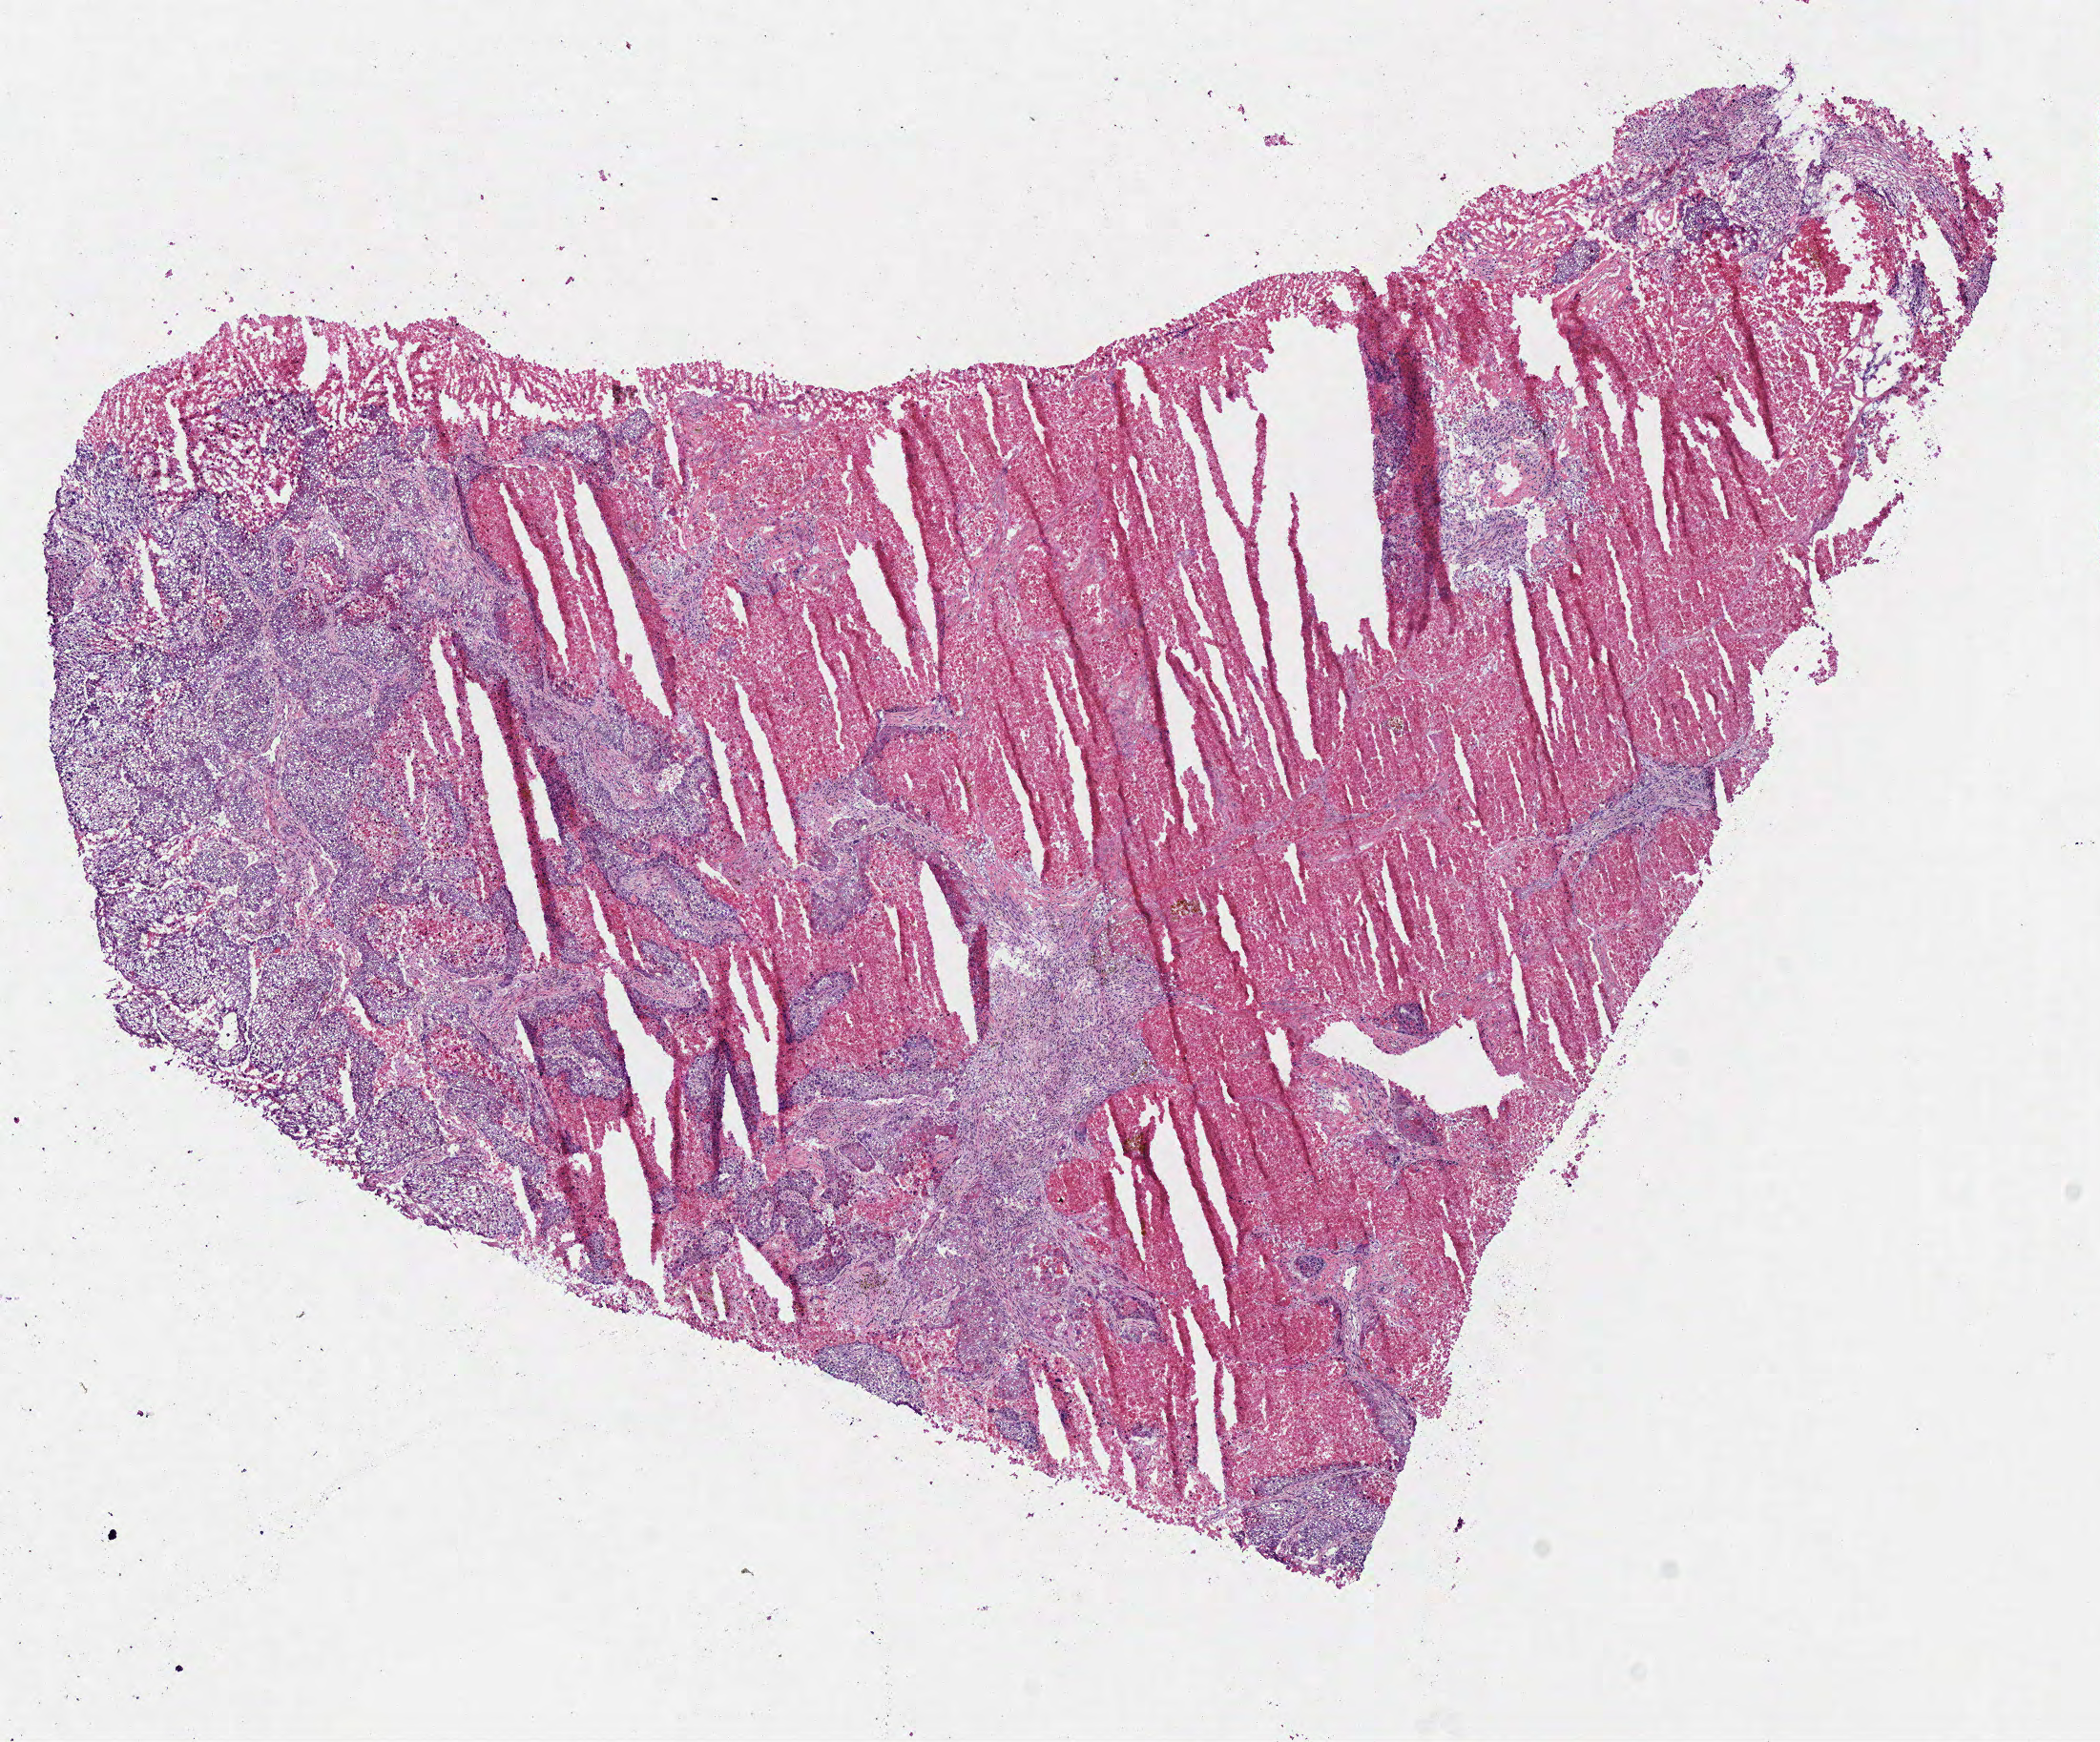
H&E-stained whole-slide image, a low-resolution overview of the entire scanned area, about 8.7 x 7.2 mm (from a 40x scan); frozen section from the bottom of the tissue portion; primary tumour sample from the lung. Male, age 69 years at initial diagnosis. Pathologist review of this section (percent, as recorded): tumour cells 30%, tumour nuclei 75%, normal cells 0%, stromal cells 10%, necrosis 60%.
- AJCC pathologic stage: IIB (6th edition)
- diagnosis: Squamous cell carcinoma, NOS (middle lobe, lung)